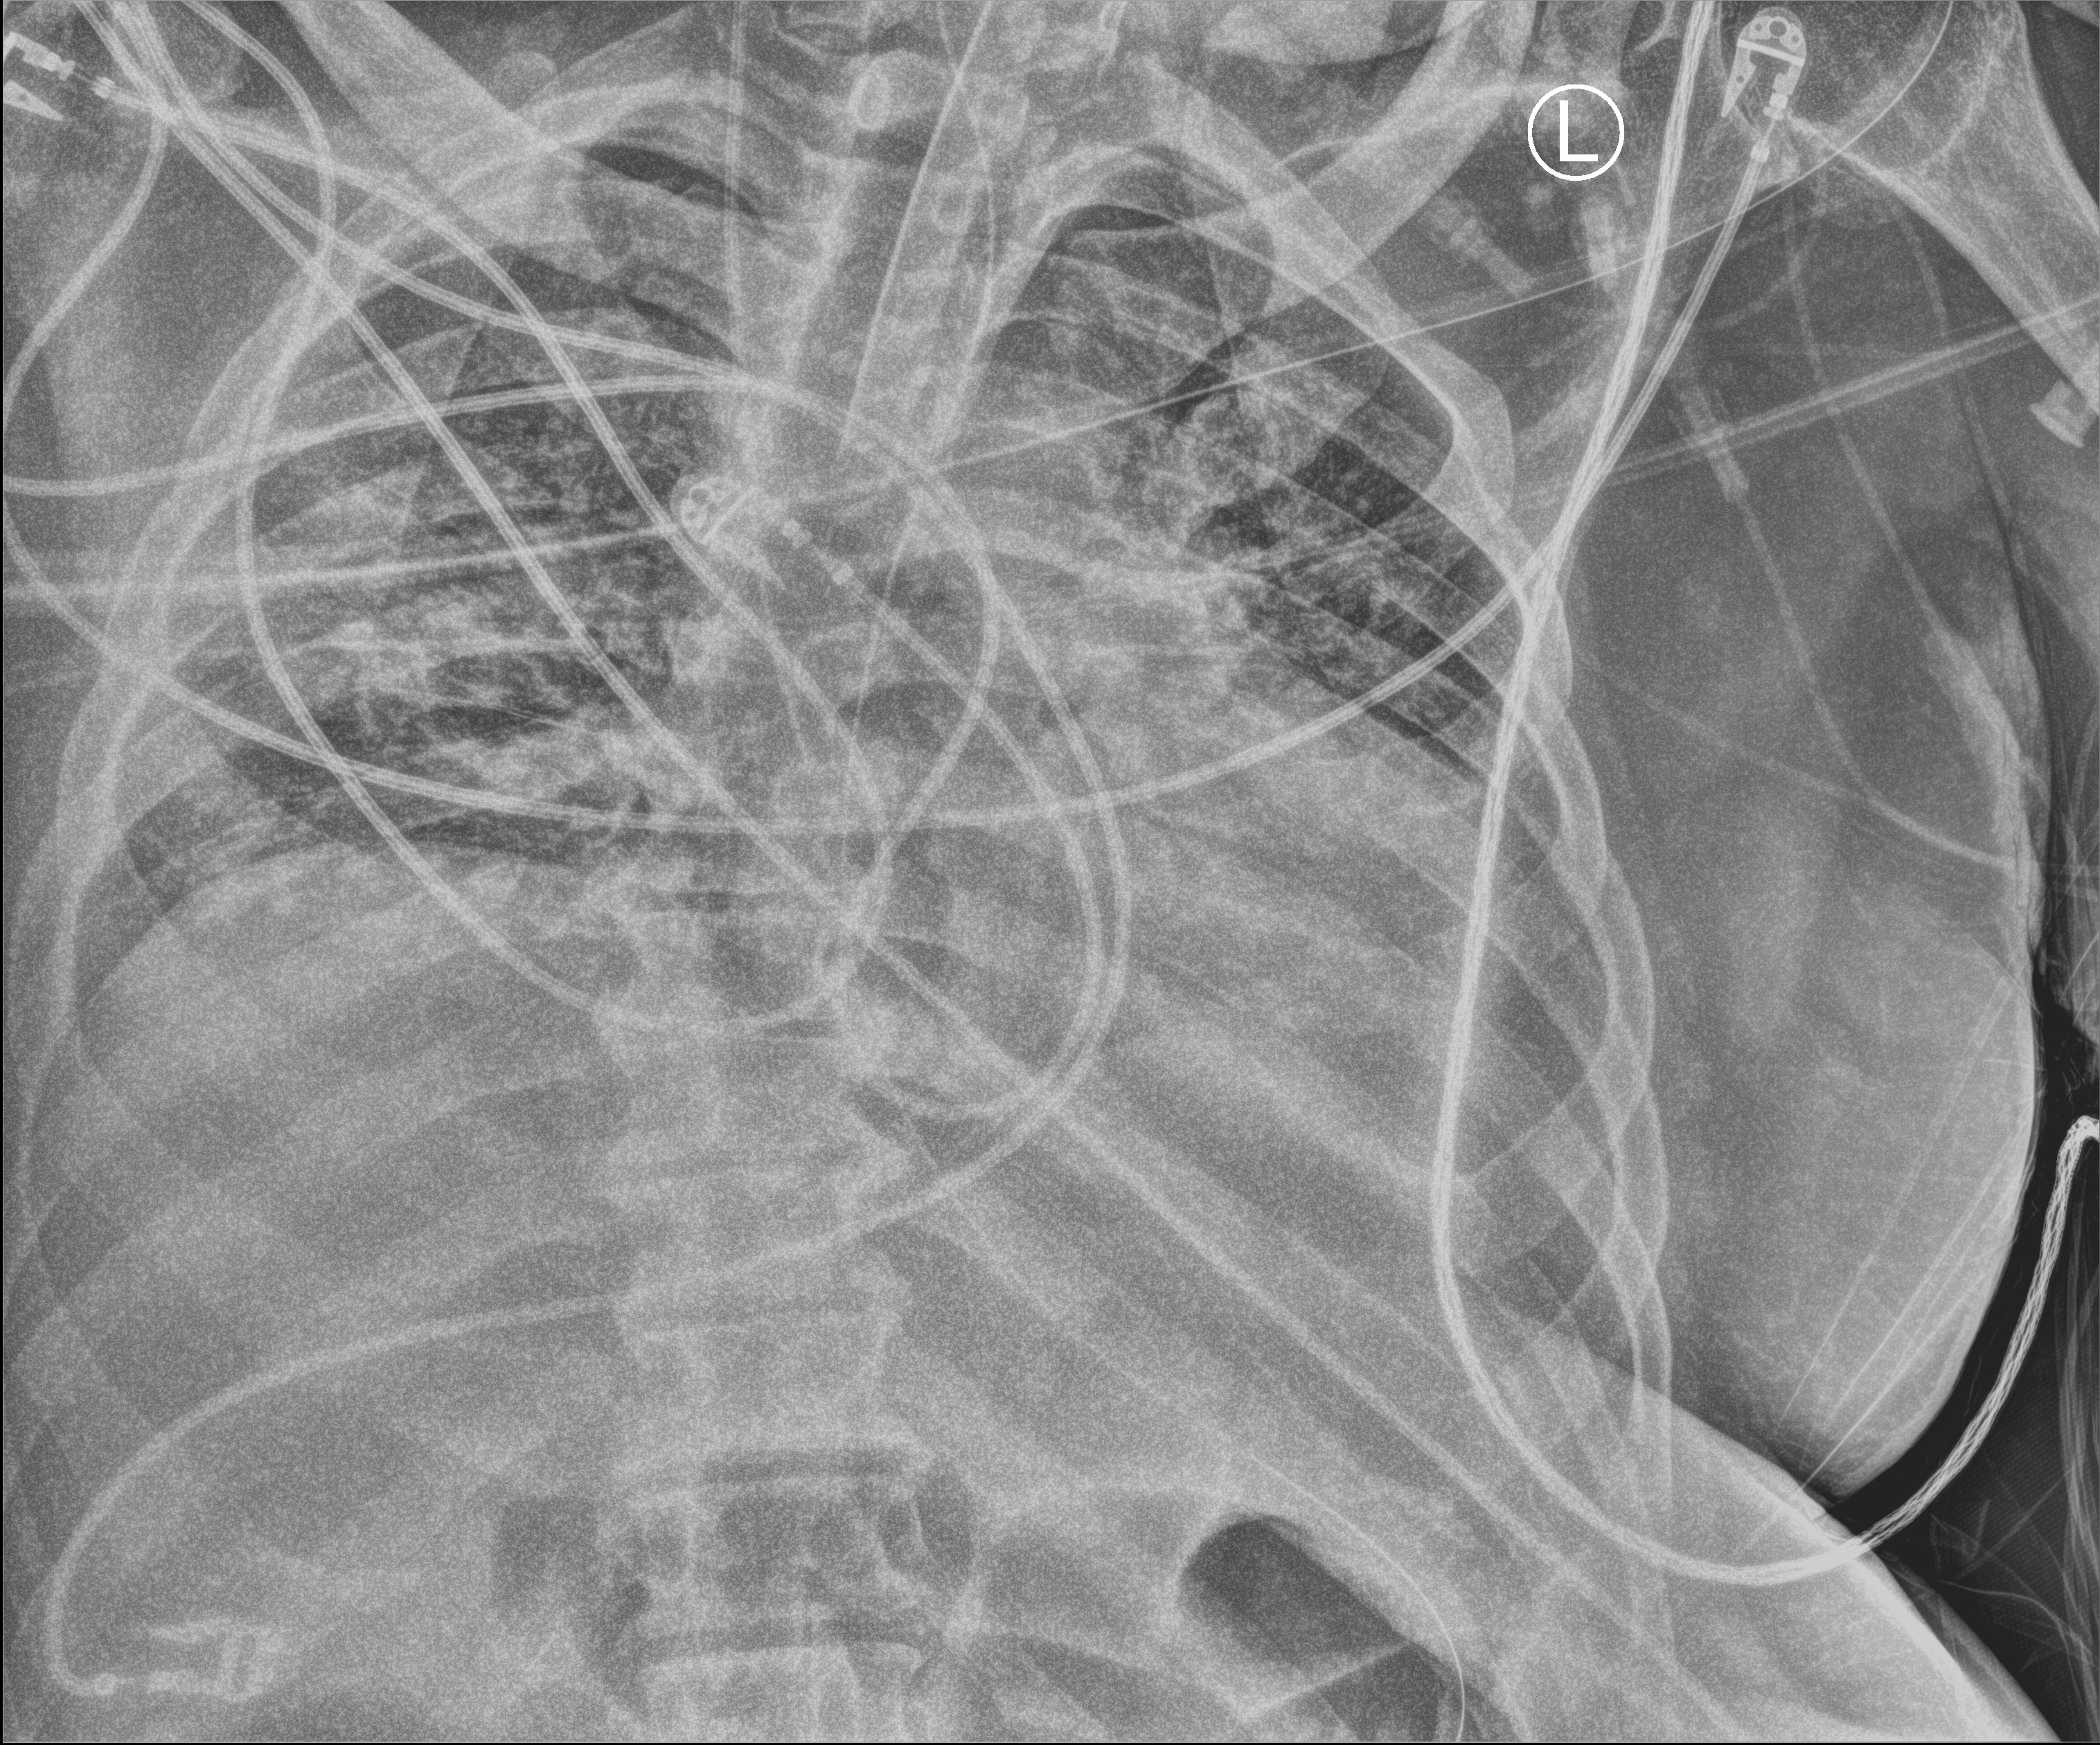
Chest X-ray (portable); anteroposterior (AP) projection. Male patient hospitalised with COVID-19, age 18–59 years.
Hospital-stay facts (about this admission, not read from this image; timing relative to this image not recorded):
- mechanically ventilated during this hospital stay: yes
- length of hospital stay: 41 days